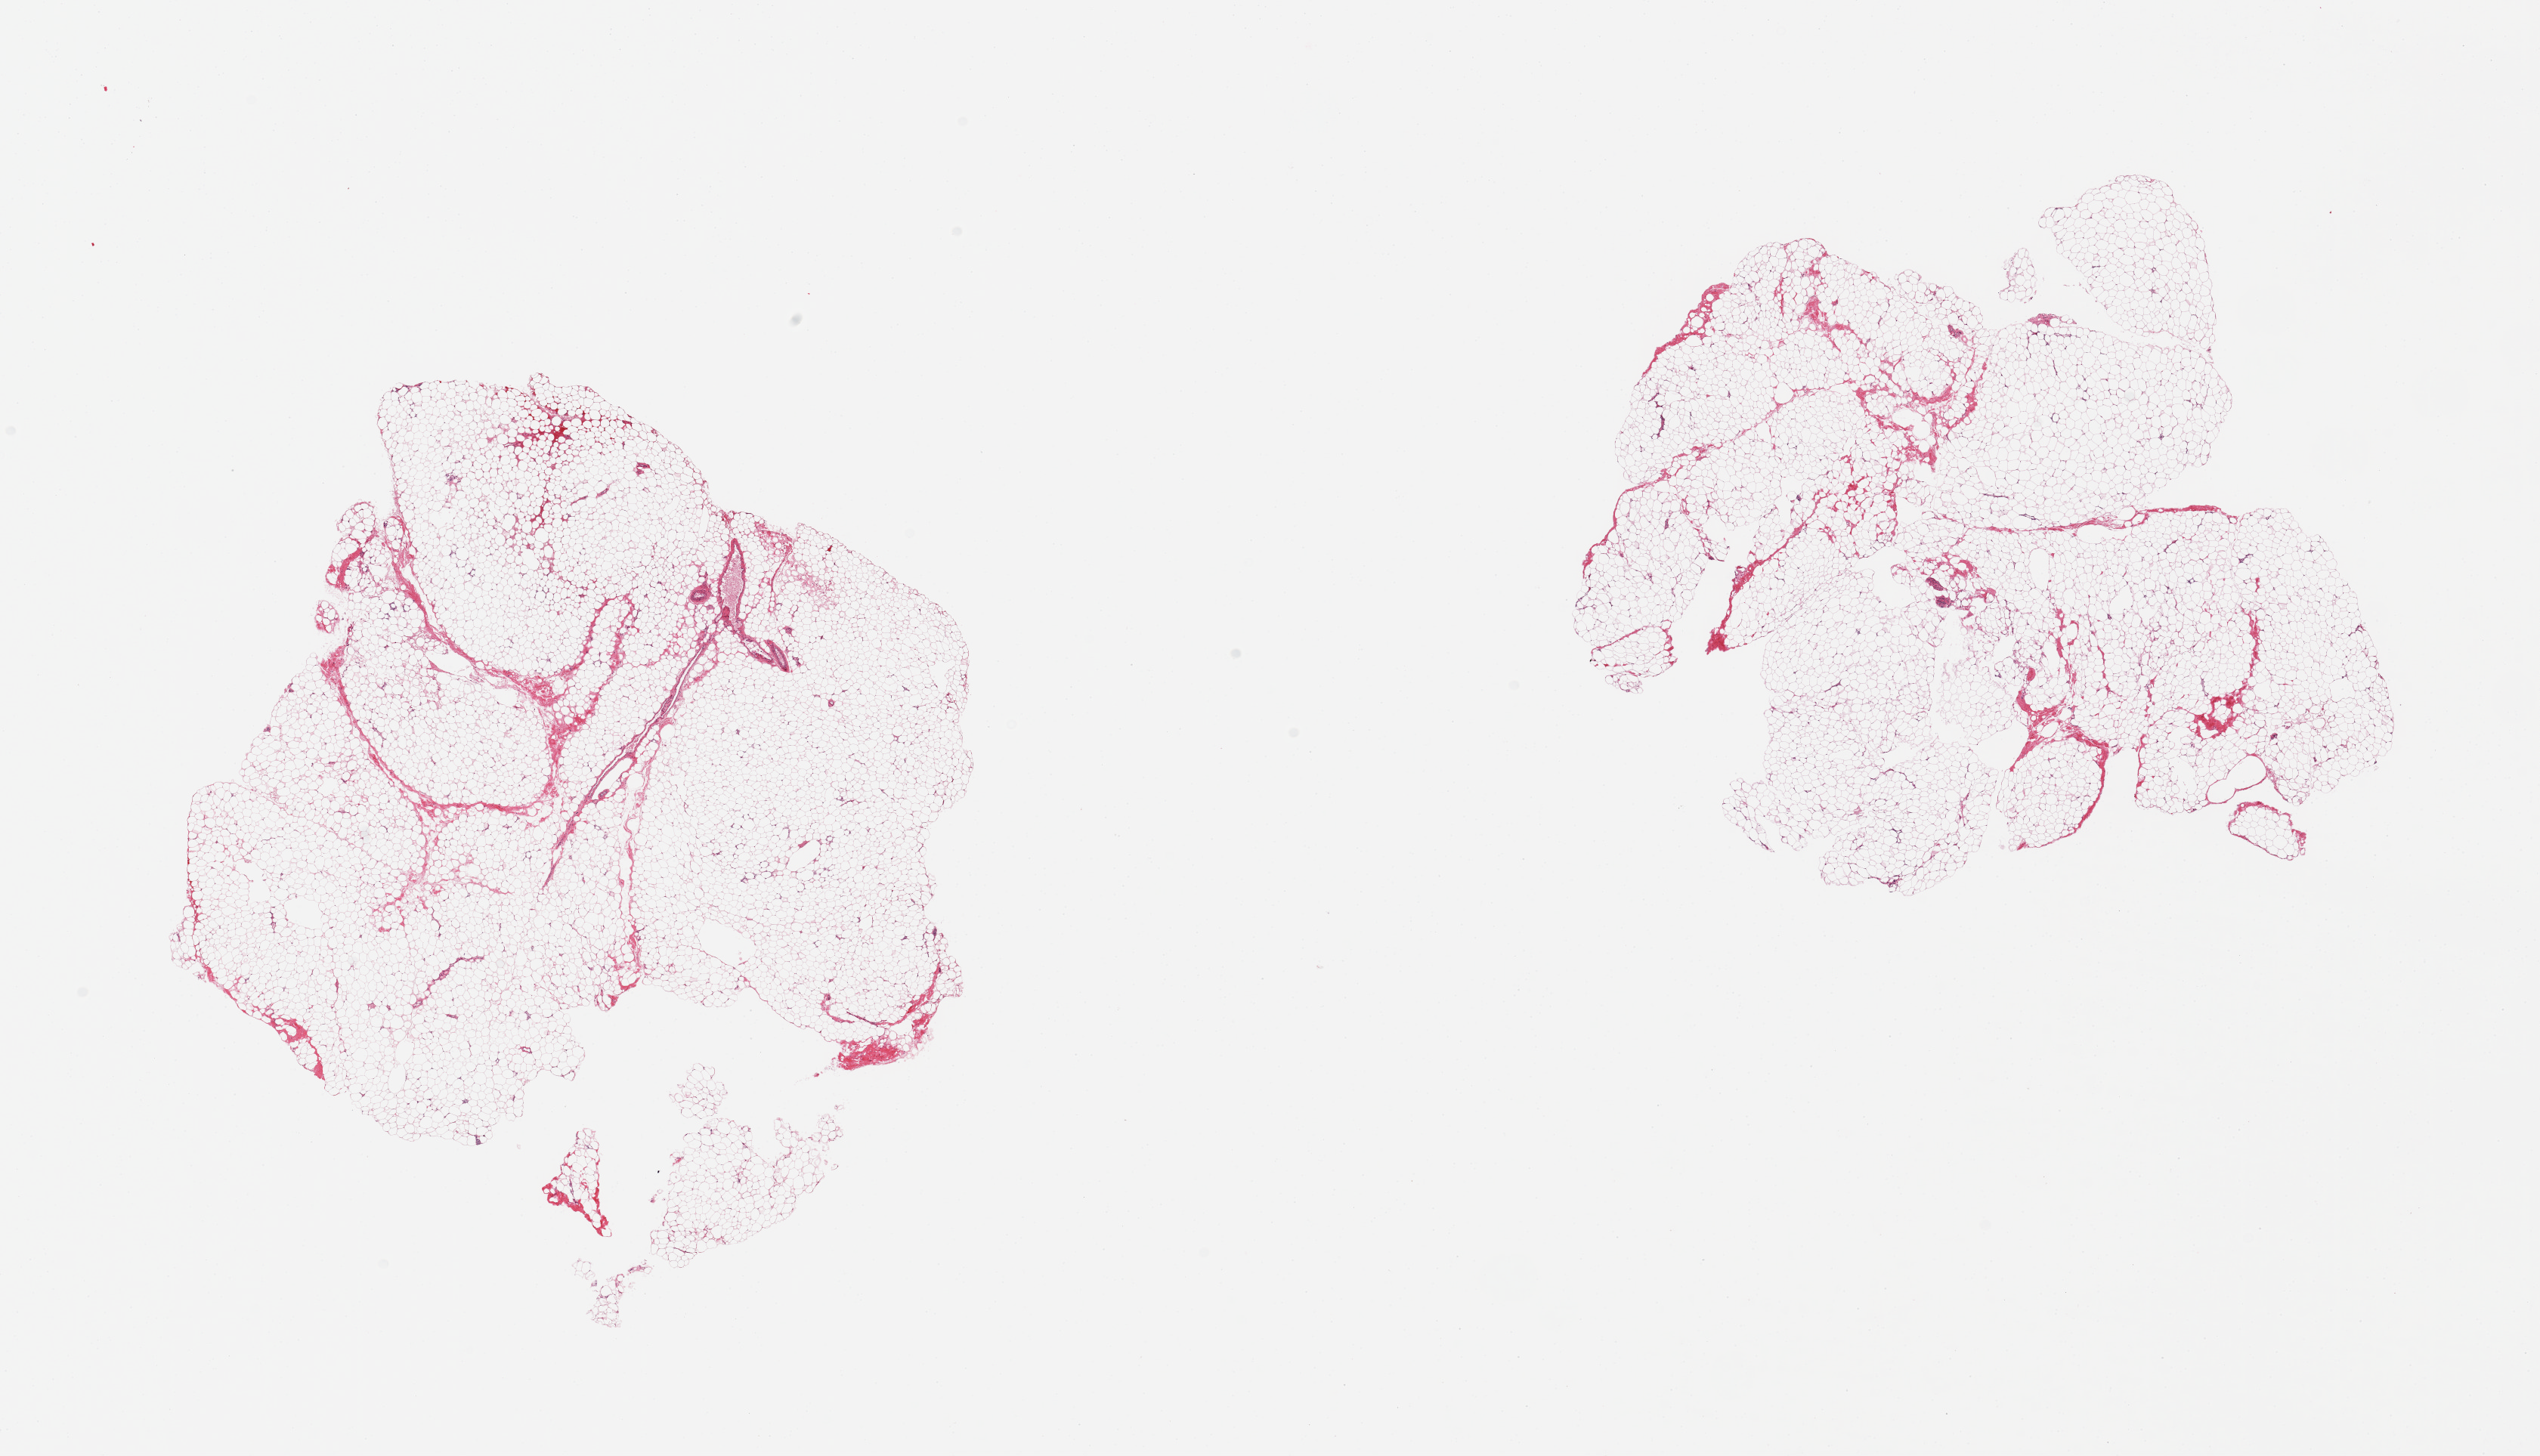
Digitized hematoxylin and eosin (H&E)-stained section — whole scanned area (about 26.6 x 15.2 mm, slide scanned at 20x) shown as a low-resolution overview, PAXgene-fixed paraffin-embedded (PFPE) section, target tissue: breast, donor tissue sample. Male donor.
Review note (as recorded): 2 pieces; adipose tissue with fibrovascular component only.